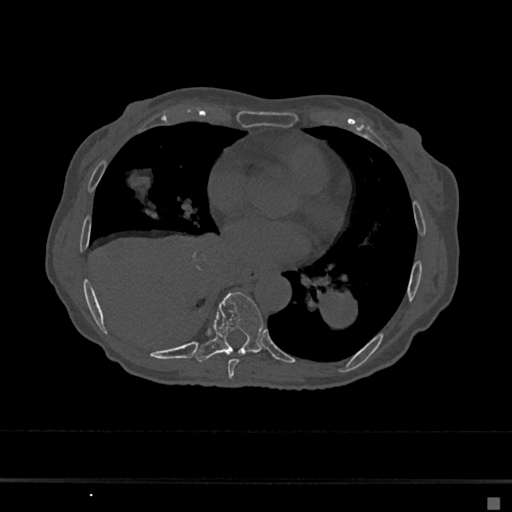
CT including the spine, one axial slice; slice 338 of 797 in the series (ordered by position); 120 kVp; bone window (W 1800 / L 400 HU); 512 × 512 image matrix, field of view 360 × 360 mm. Female patient, age 68 years. From the clinical record (not read from this slice): primary cancer: renal.
Outlined on this slice (semi-automatic segmentation, software-assisted and operator-edited):
- T7 vertebra: bounding box <228,359,239,378> (left, top, right, bottom; pixels)
- T8 vertebra: <196,292,264,362>